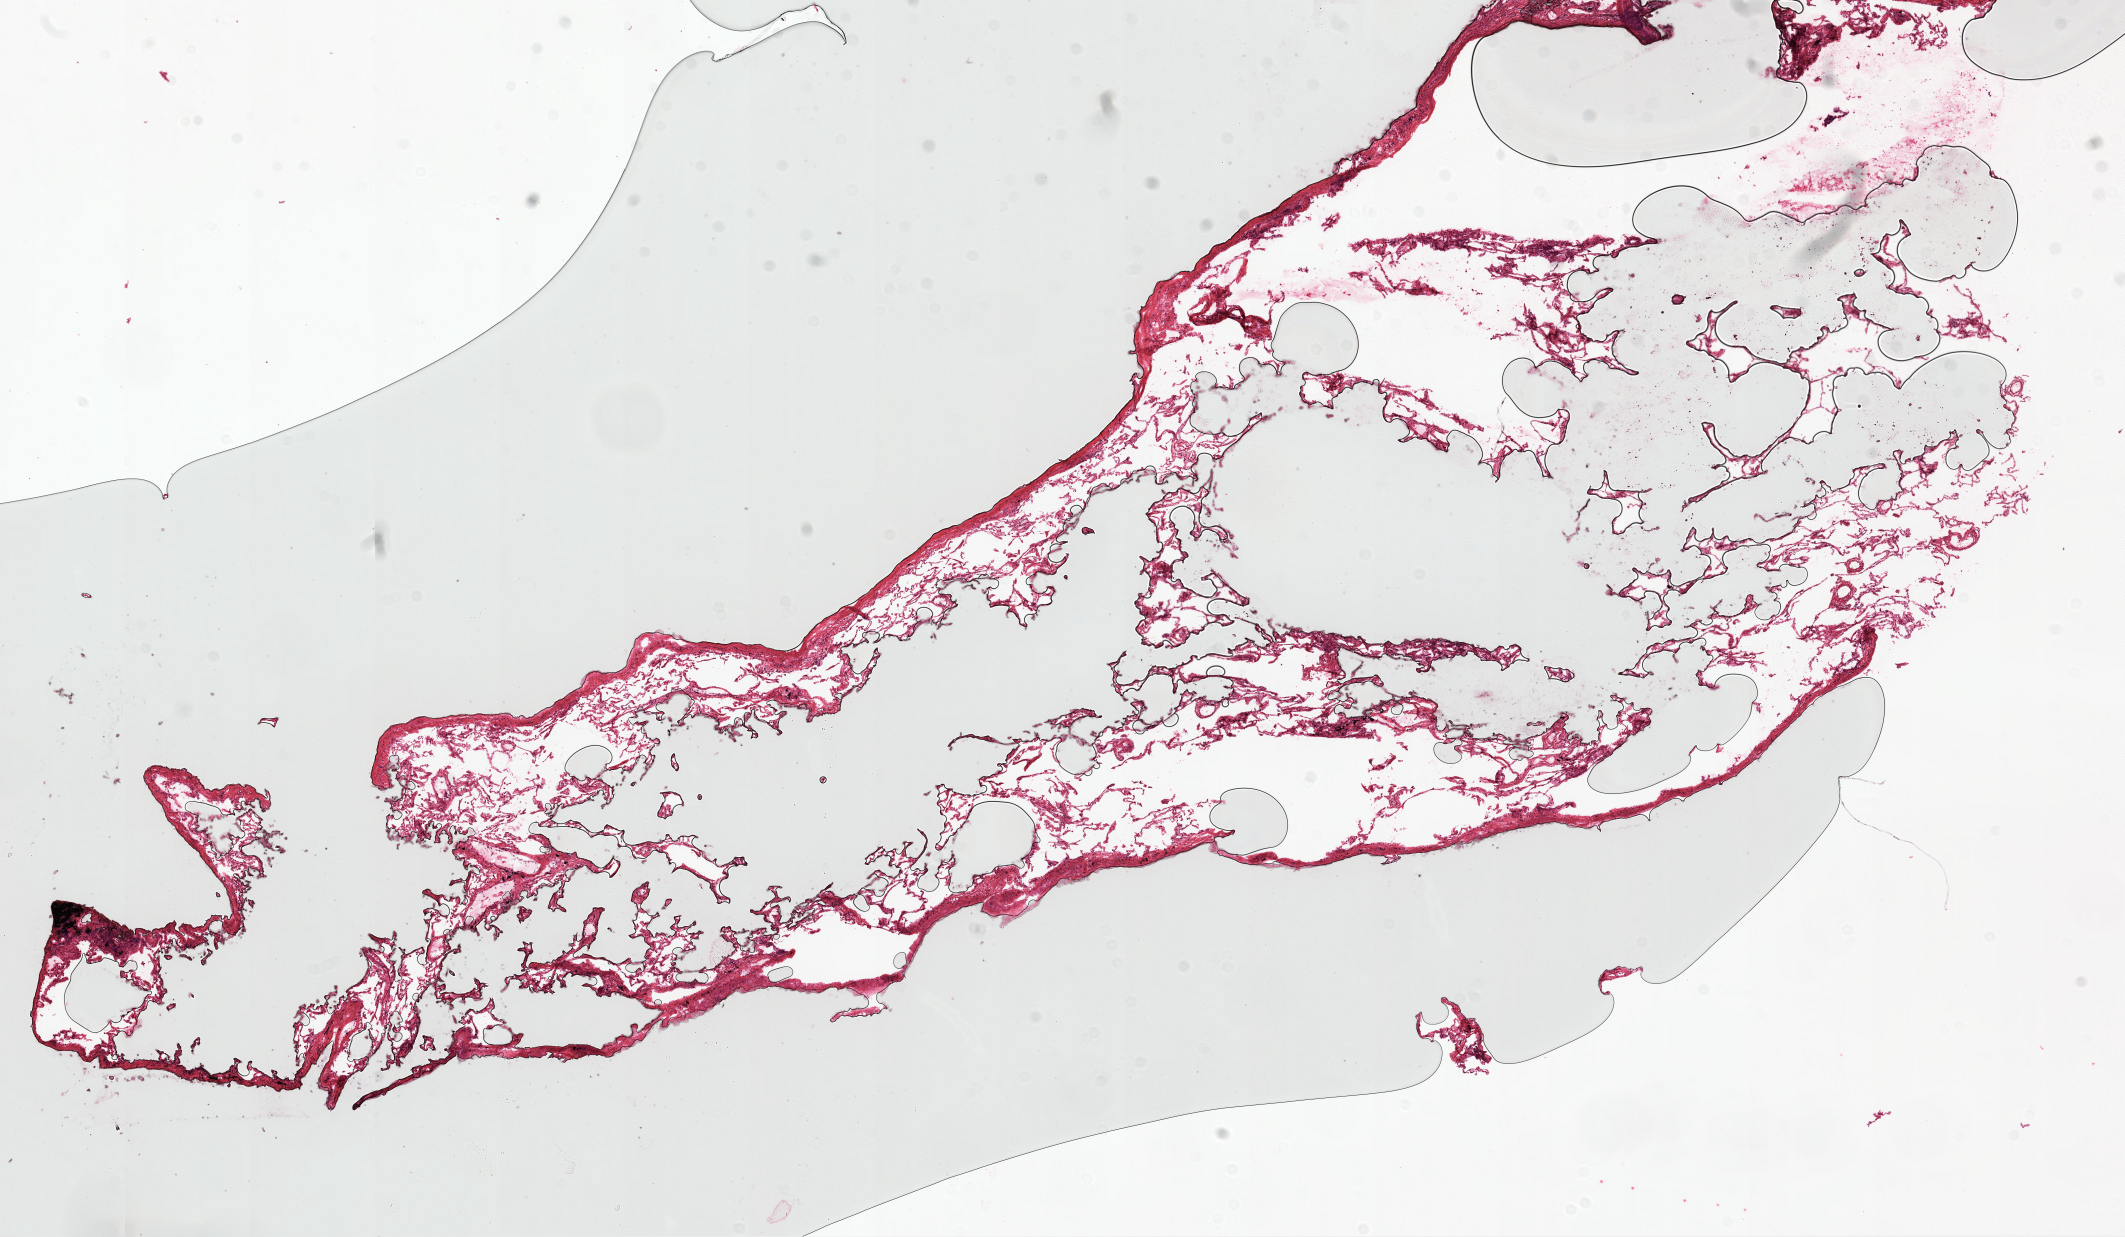
Whole-slide histology image, H&E-stained — shown as a low-resolution overview of the whole scanned area (about 17.1 x 9.9 mm, from a 20x scan). Frozen section from the top of the tissue portion. Sample: solid tissue normal (non-tumour tissue), lung. Male patient; age at initial diagnosis 81 years.
This section: solid tissue normal (non-tumour) sample from the same patient. Patient diagnosis: Squamous cell carcinoma, NOS (lower lobe, lung).